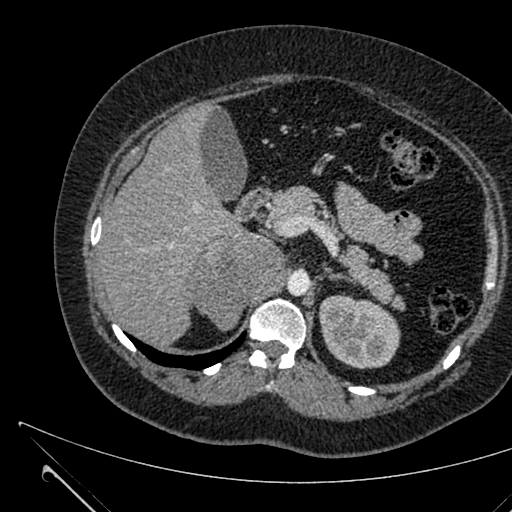
Contrast-enhanced abdominal CT, one axial slice; position 425 of 731 along the scan axis; intravenous contrast given; soft-tissue window (W 400 / L 40 HU); 1 mm slice thickness; 512 × 512 image matrix. Patient: female, 36 years. Case-level facts recorded for this patient, not image findings: diagnosis: adrenocortical carcinoma; tumour side: right adrenal; tumour size at pathology: 10 cm; Ki-67 index: 20 %; stage (as recorded): 4.
Outlined on this slice (semi-automatically segmented with operator editing):
- mass: bounding box [x1, y1, x2, y2] px = [190, 235, 283, 328]